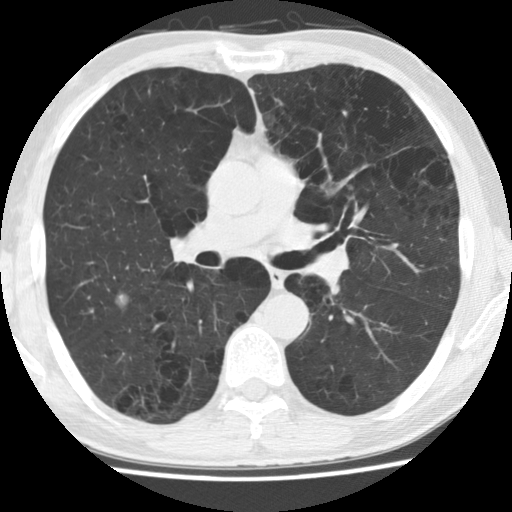
Chest CT (low-dose screening protocol), one axial image; baseline annual screen; lung window (W 1500 / L -600 HU); 120 kVp; 512 × 512 image matrix. Male, age 62 years at enrolment. Current smoker at enrolment.
- Expert-annotated lung lesion, box from (x=87, y=267) to (x=148, y=330) px.
- The screening reader recorded 2 non-calcified nodules or masses ≥4 mm on this exam (left upper lobe, right upper lobe); which of them this box marks is not recorded.
- Official screen result: positive, change unspecified: nodule(s) >= 4 mm or enlarging nodule(s), mass(es), or other non-specific abnormalities suspicious for lung cancer.